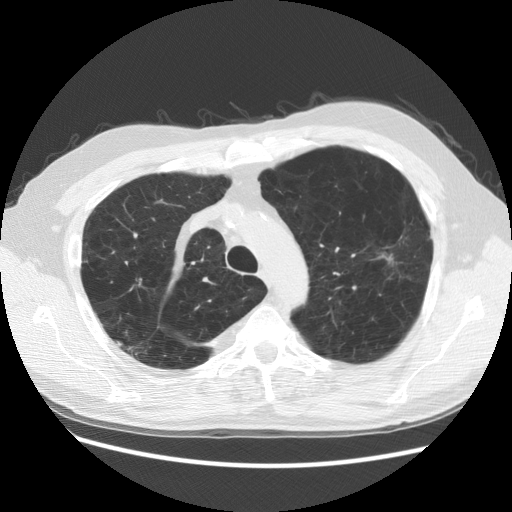
Axial slice from a low-dose chest CT screening exam. Third annual screen. Lung window (W 1500 / L -600 HU). 2.5 mm slice thickness. 140 kVp. 512 × 512 image matrix, field of view 377 × 377 mm. Male, age 58 years at enrolment. Former smoker at enrolment.
• Lesion marked by an expert reader, bounding box <114,259,154,308> (left, top, right, bottom; pixels).
• The screening reader recorded 3 non-calcified nodules or masses ≥4 mm on this exam (right lower lobe, right upper lobe, right upper lobe); which of them this box marks is not recorded.
• Lung cancer was diagnosed 88 days after this screen: squamous cell carcinoma, NOS, right upper lobe, moderately differentiated (G2), stage IB (AJCC 6th edition), 18 mm at pathology.